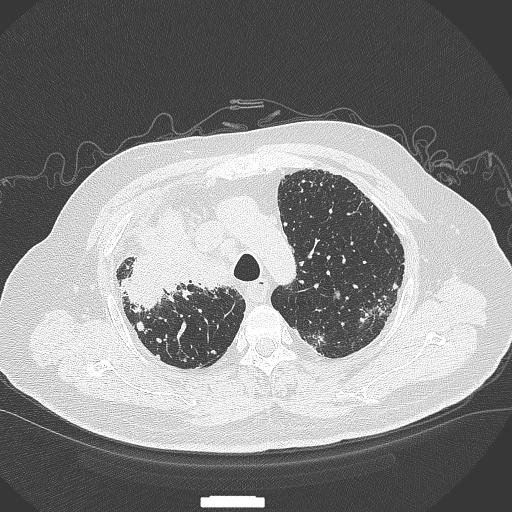
Chest CT, one axial slice; slice 278 of 384 in the series (ordered by position); reconstruction kernel B70f; 120 kVp; lung window (W 1500 / L -600 HU); 1 mm slice thickness; 512 × 512 image matrix. Male patient, age 69 years. From the clinical record (not read from this slice): clinical TNM (as recorded): T4 N3 M1.
Structures marked on this image (rectangle marked by the reading radiologist):
- lung tumour (recorded histology: adenocarcinoma): bounding box (x1, y1, x2, y2) in pixels: (119, 206, 230, 317)